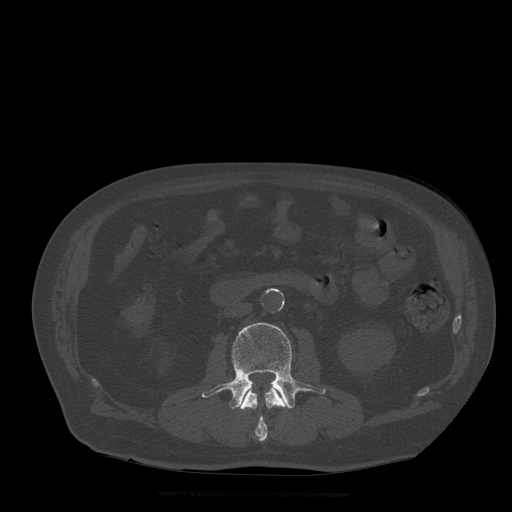
CT including the spine, one axial slice. Slice 150 of 522 in the series (ordered by position). Bone window (W 1800 / L 400 HU). 1.25 mm slice thickness. 512 × 512 image matrix. Patient age 72 years. From the clinical record (not read from this slice): primary cancer: prostate.
Structures marked on this image (semi-automatic segmentation, software-assisted and operator-edited):
- L2 vertebra: box from (x=241, y=386) to (x=287, y=442) px
- L3 vertebra: (x=202, y=323)–(x=326, y=409)